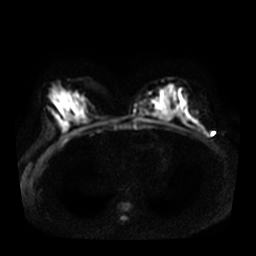
Breast MRI, one axial slice; position 15 of 30 along the scan axis; diffusion-weighted series; image 2 of 4 stored at this slice position (different b-values; order by instance number); 3 T; 256 × 256 image matrix. Female patient.
Outlined on this slice (expert manual segmentation):
- tumour on diffusion-weighted imaging: bounding box <202,130,206,135> (left, top, right, bottom; pixels)